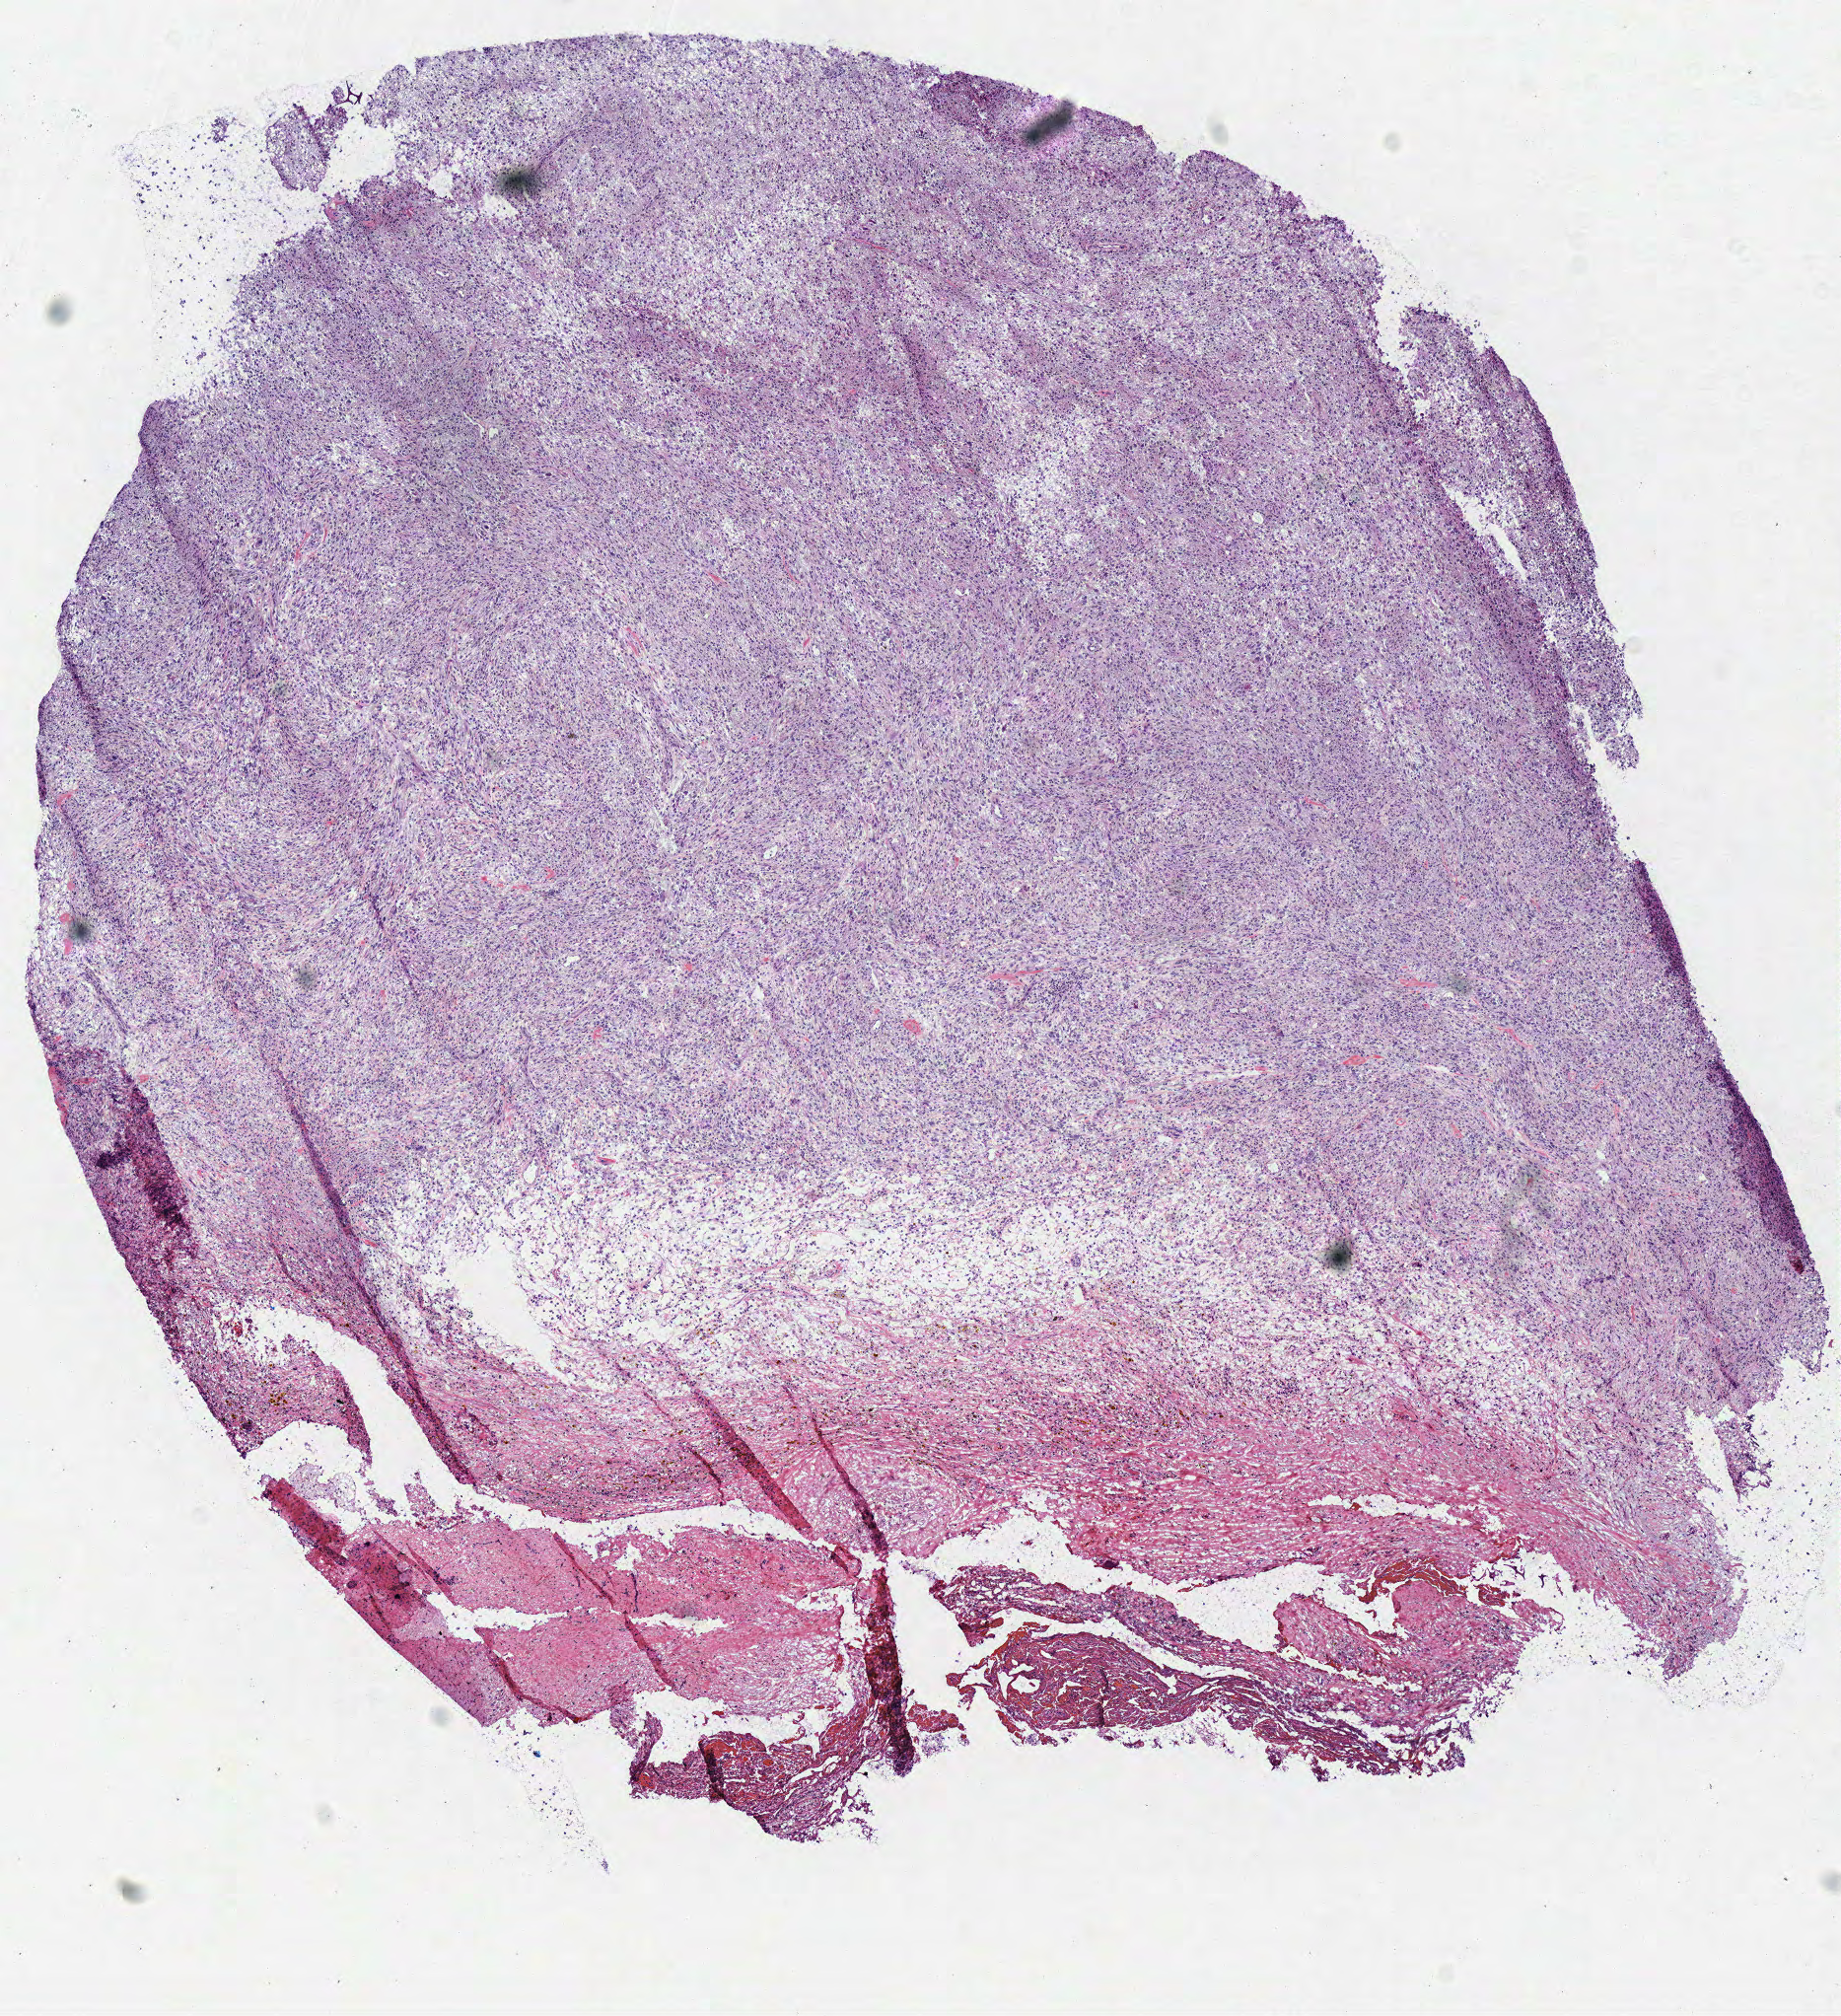
Digitized H&E tissue section (whole slide), a low-resolution overview of the entire scanned area, about 7.3 x 8.0 mm (from a 40x scan), frozen section from the bottom of the tissue portion, primary tumour sample from the brain. Male patient; age at initial diagnosis 65 years. Composition of this section per pathologist review: tumour cells 90%, tumour nuclei 80%, normal cells 0%, stromal cells 10%, necrosis 0%.
Diagnosis: Glioblastoma.